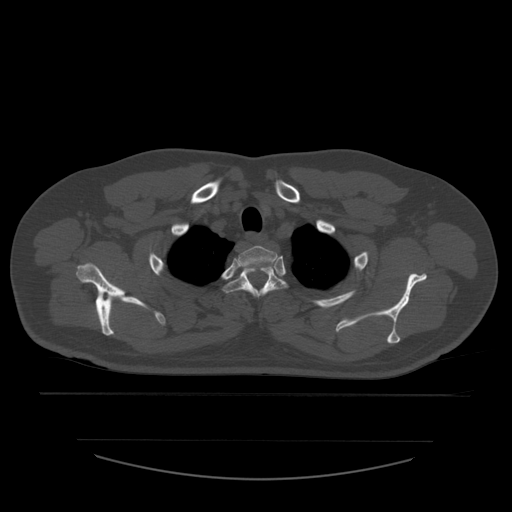
CT including the spine, one axial slice. Bone window (W 1800 / L 400 HU). 512 × 512 image matrix, field of view 441 × 441 mm. Patient age 44 years. From the clinical record (not read from this slice): primary cancer: soft tissue sarcoma.
Structures marked on this image (semi-automatic segmentation, software-assisted and operator-edited):
- T1 vertebra: box from (x=237, y=246) to (x=278, y=269) px
- T2 vertebra: (x=224, y=266)–(x=287, y=298)